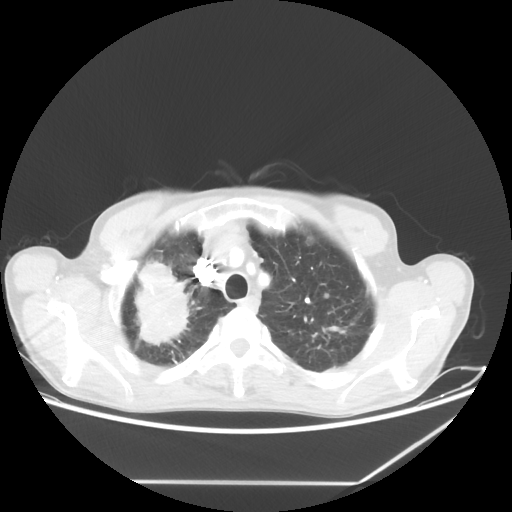
Chest CT, one axial slice. Slice 53 of 65 in the series (ordered by position). Reconstruction kernel STANDARD. Lung window (W 1500 / L -600 HU). 5 mm slice thickness. 512 × 512 image matrix, field of view 397 × 397 mm. Male patient, age 68 years. From the clinical record (not read from this slice): clinical TNM (as recorded): T3 N3 M0.
Structures marked on this image (bounding box drawn by a radiologist):
- lung tumour (recorded histology: adenocarcinoma): bounding box (x1, y1, x2, y2) in pixels: (119, 248, 200, 355)